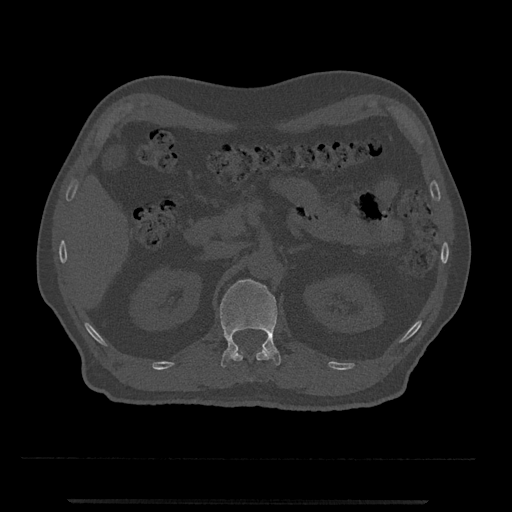
CT including the spine, one axial slice. Slice 360 of 797 in the series (ordered by position). Reconstruction kernel Br40s/3. 120 kVp. Bone window (W 1800 / L 400 HU). 0.5 mm slice thickness. 512 × 512 image matrix, field of view 419 × 419 mm. Male patient, age 63 years. Case-level facts recorded for this patient, not image findings: primary cancer: prostate.
Structures marked on this image (semi-automatic segmentation, software-assisted and operator-edited):
- L1 vertebra: bounding box <220,279,281,367> (left, top, right, bottom; pixels)
- T12 vertebra: <231,347,271,381>